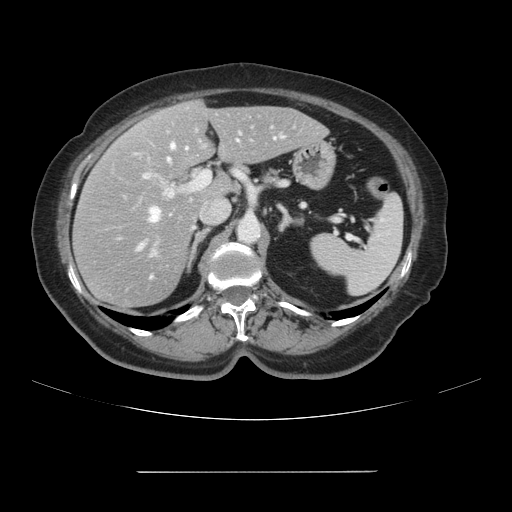
Contrast-enhanced abdominal CT, one axial slice. Position 60 of 111 along the scan axis. Intravenous contrast given. Soft-tissue window (W 400 / L 40 HU). 2.5 mm slice thickness. 512 × 512 image matrix. Female patient, age 74 years. From the clinical record (not read from this slice): diagnosis: colorectal cancer liver metastases, imaged before liver resection; multiple liver metastases: yes; largest metastasis: 1.1 cm; disease in both lobes: yes.
Annotated regions visible in this slice (manually delineated by an expert):
- hepatic veins: bounding box <140,137,276,247> (left, top, right, bottom; pixels)
- liver: <75,101,326,309>
- planned liver remnant (the part of the liver to remain after resection): <146,101,326,197>
- portal vein (with intrahepatic branches): <142,125,318,255>